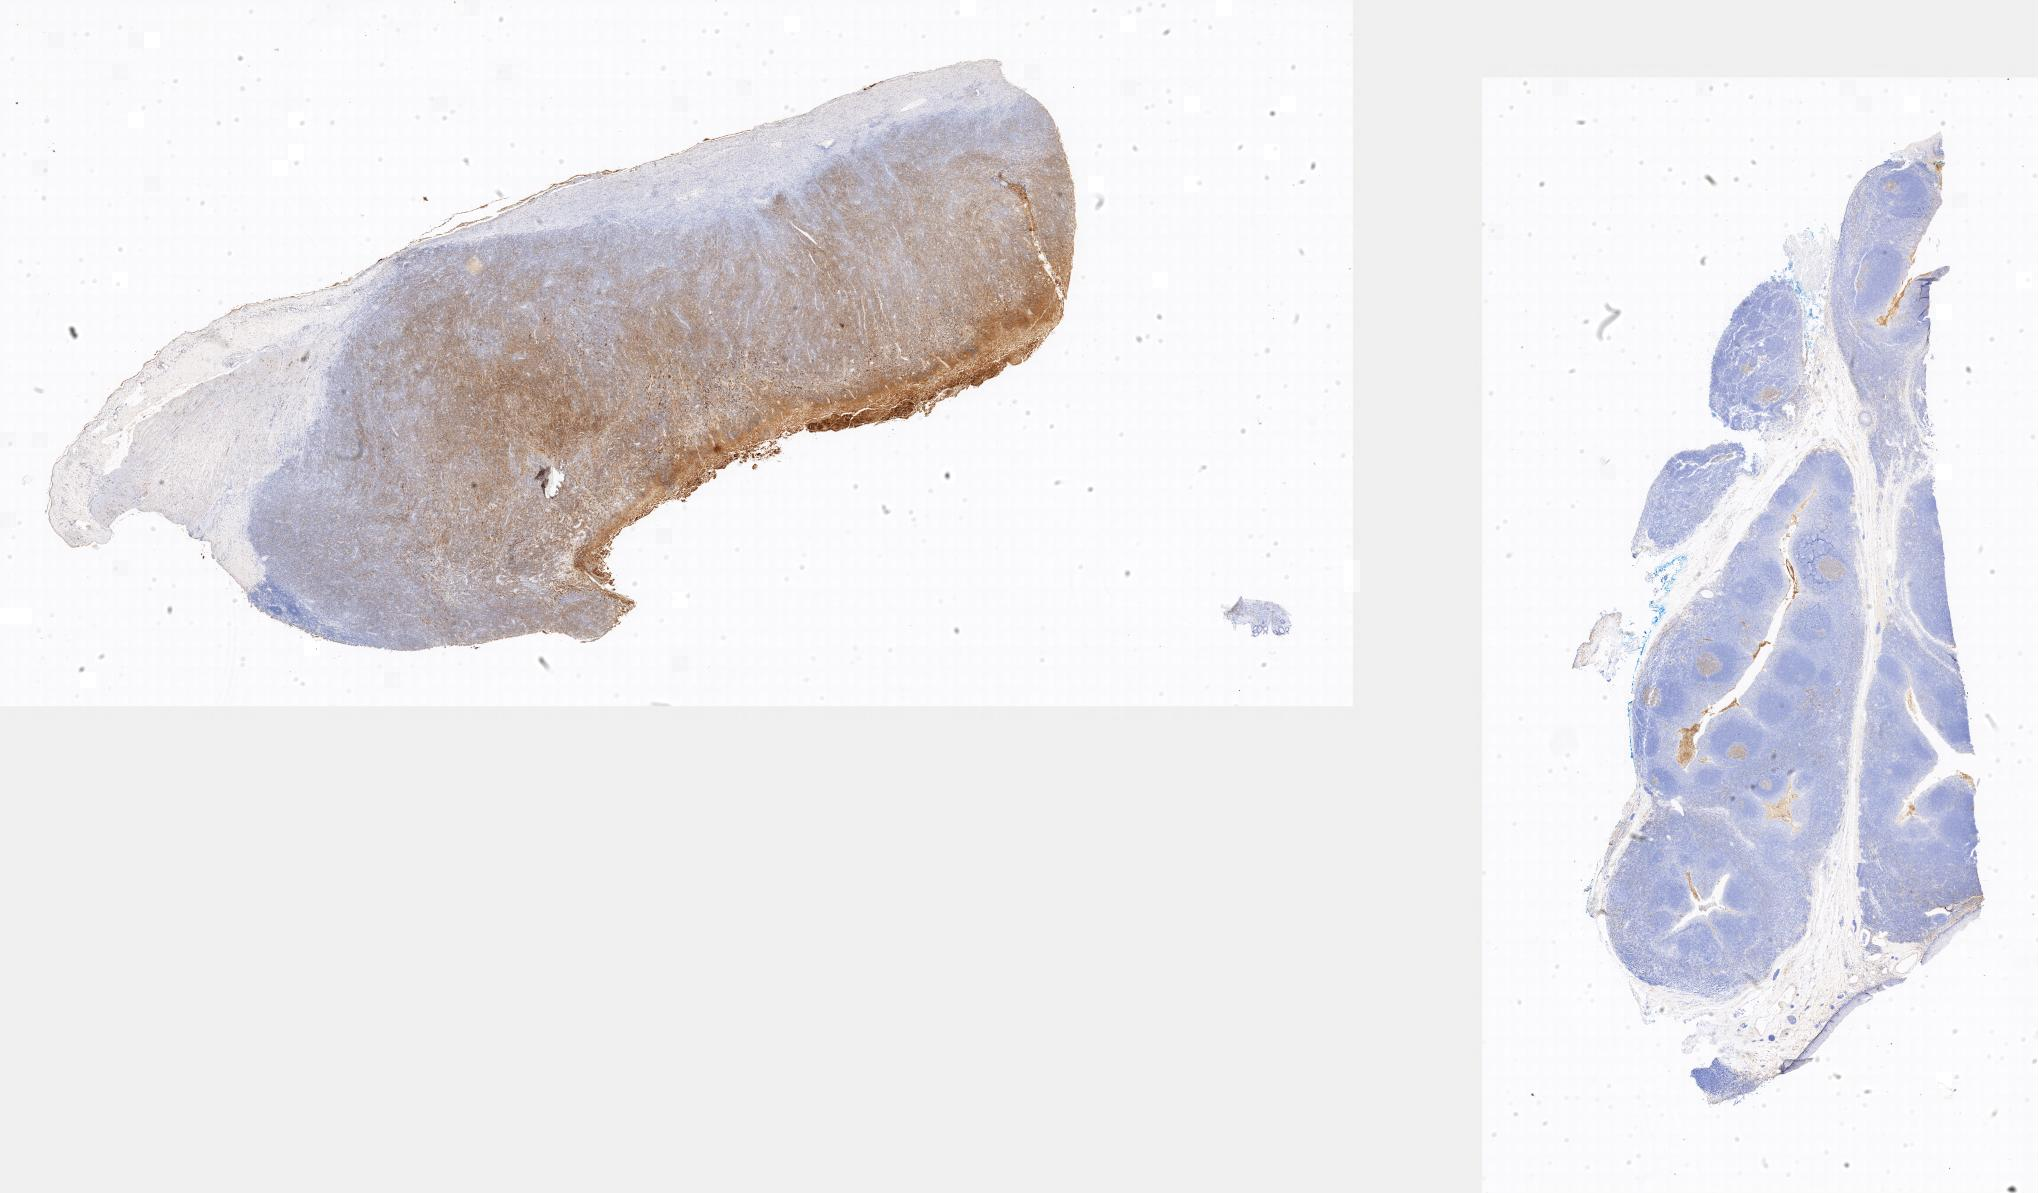
IHC for CD10, whole-slide image — a low-resolution overview of the entire scanned area, specimen: tumor tissue, site: small intestine. Male, age 3 years at initial diagnosis.
Histologic diagnosis: Burkitt lymphoma, NOS.